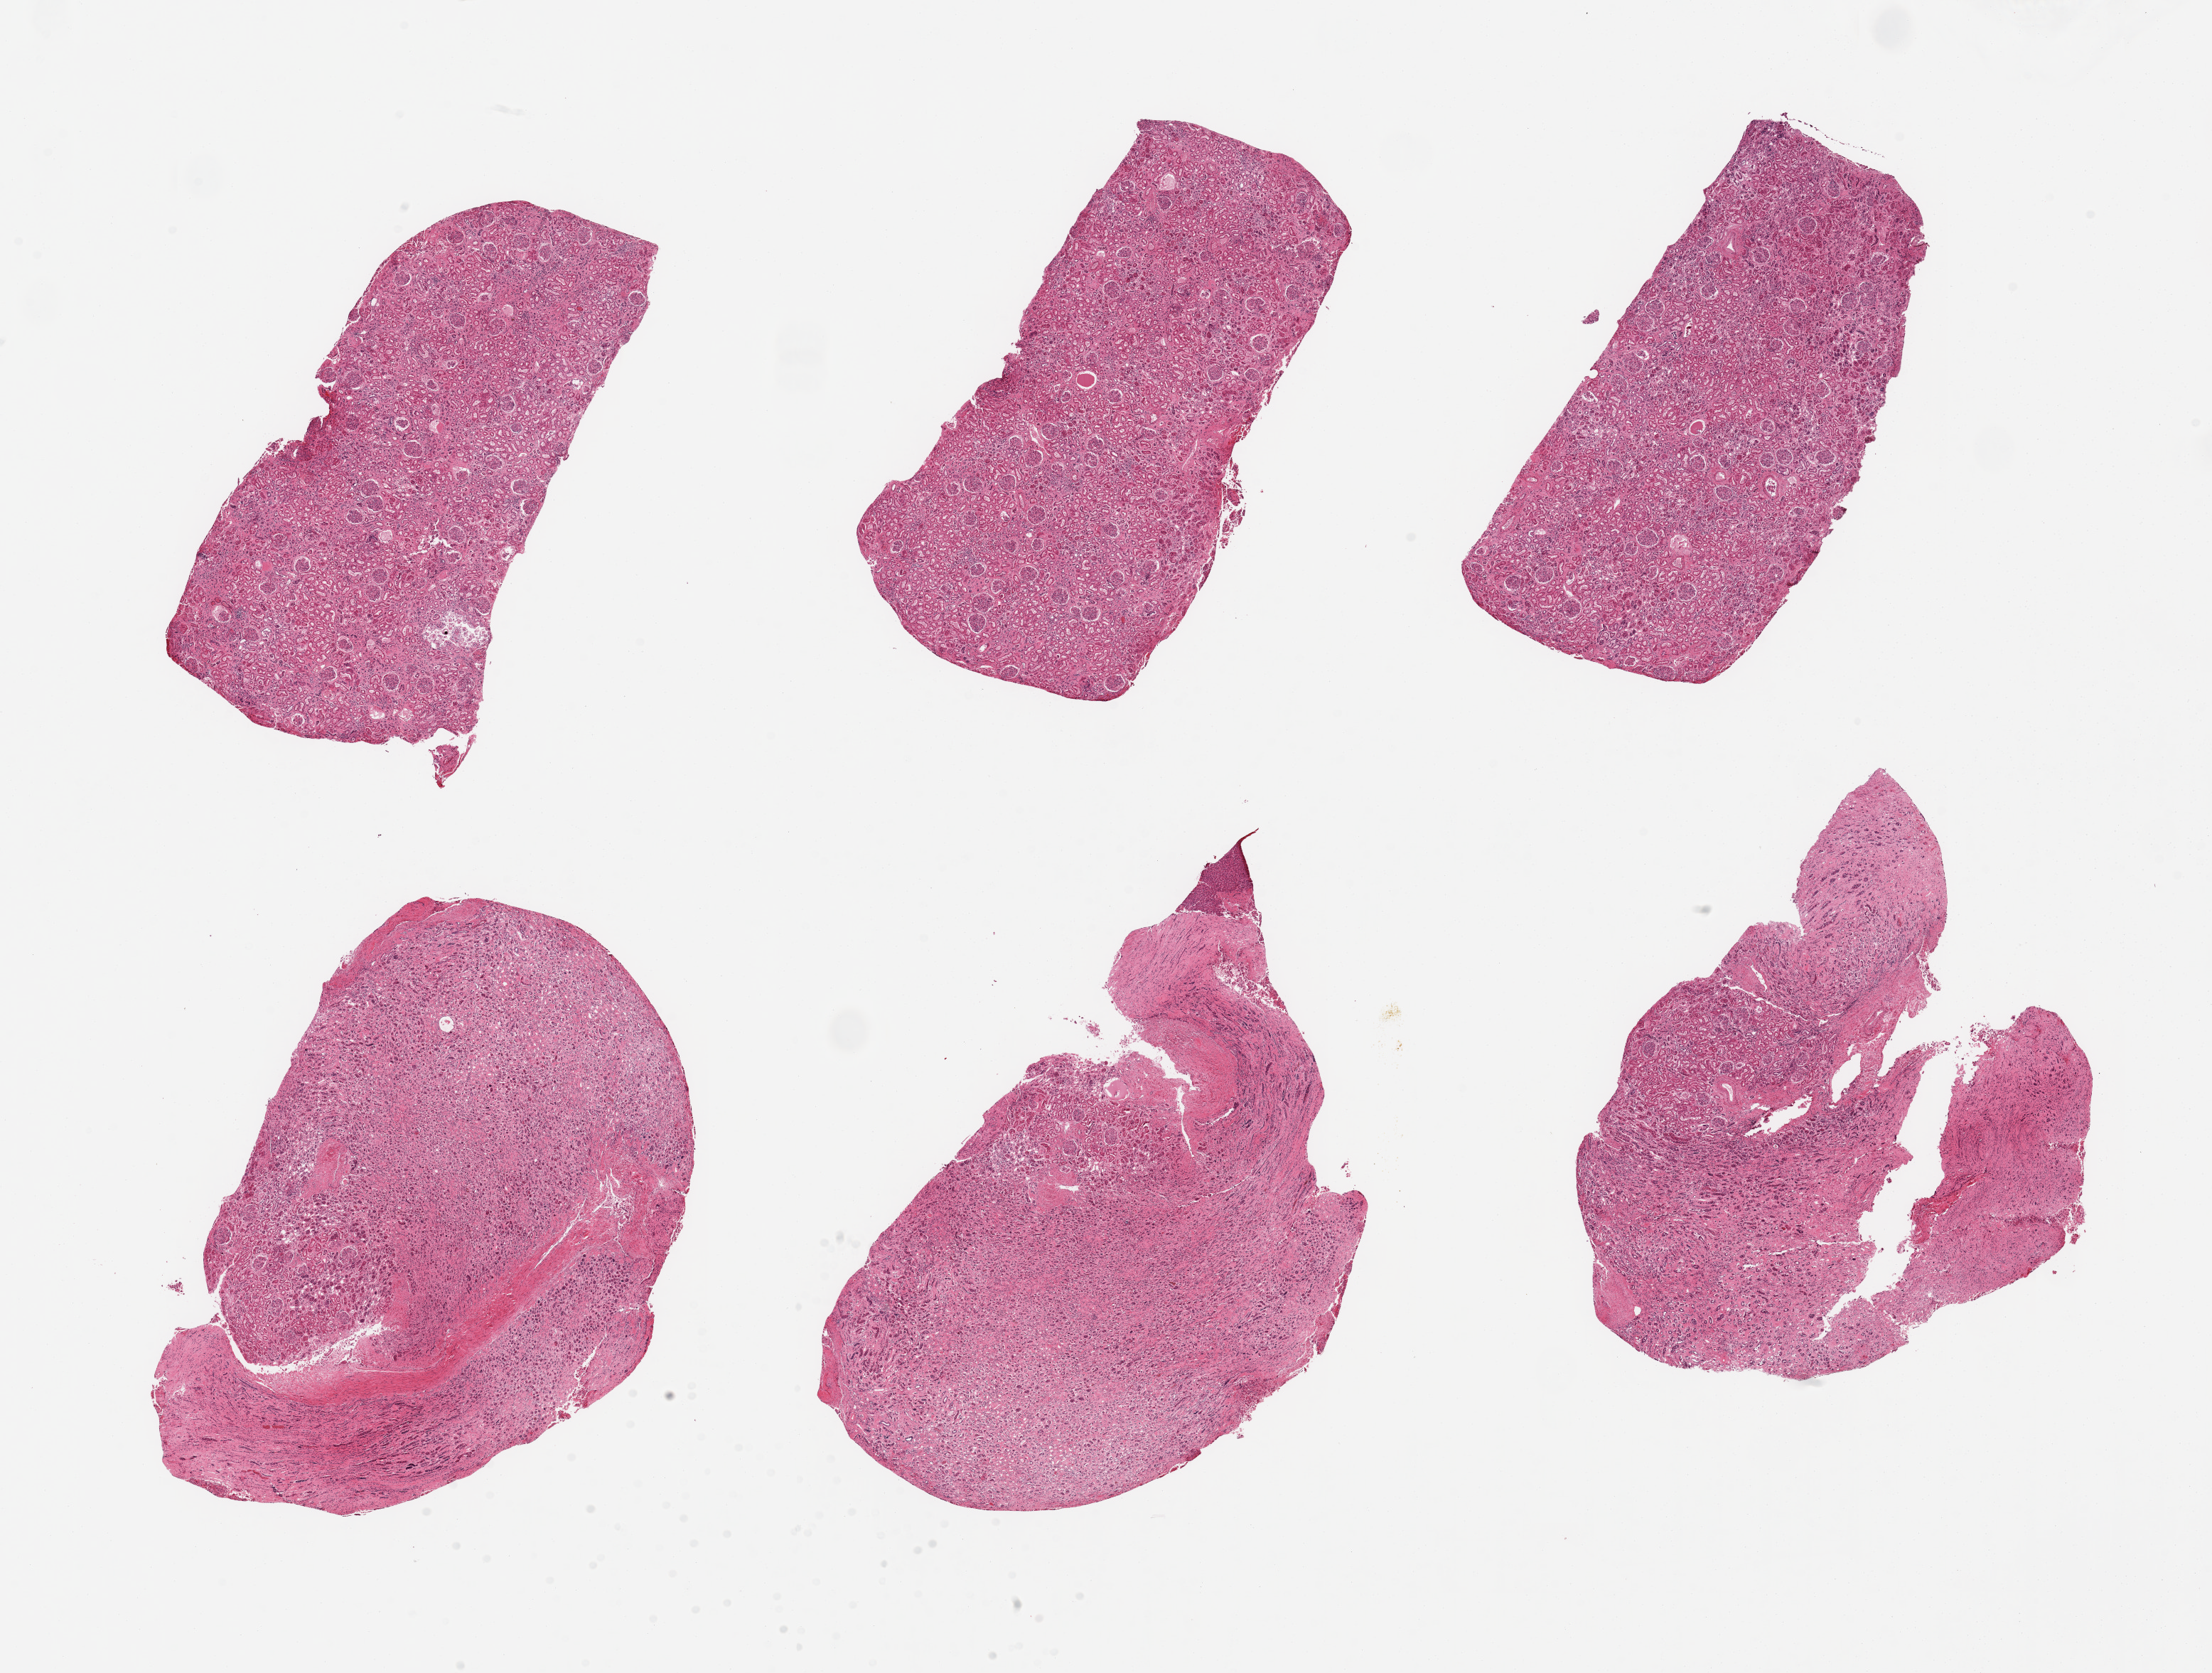
Whole-slide image, hematoxylin and eosin (H&E) stain, whole scanned area (about 24.6 x 18.6 mm, acquisition: 20x scan) shown as a low-resolution overview; PAXgene-fixed paraffin-embedded (PFPE) section; target tissue: renal cortex; donor tissue sample. Donor: male.
Review note (as recorded): 6 pieces, glomeruli present; tubules iwth mild-moderate autolysis.